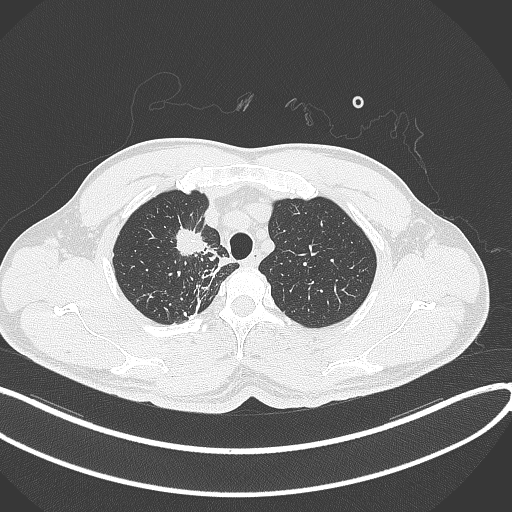
Chest CT, one axial slice; slice 314 of 391 in the series (ordered by position); reconstruction kernel B70f; 120 kVp; lung window (W 1500 / L -600 HU); 512 × 512 image matrix, field of view 400 × 400 mm. Male patient, age 48 years. Case-level facts recorded for this patient, not image findings: clinical TNM (as recorded): T1c N1 M1.
Structures marked on this image (rectangle marked by the reading radiologist):
- lung tumour (recorded histology: adenocarcinoma): bounding box <171,223,207,262> (left, top, right, bottom; pixels)